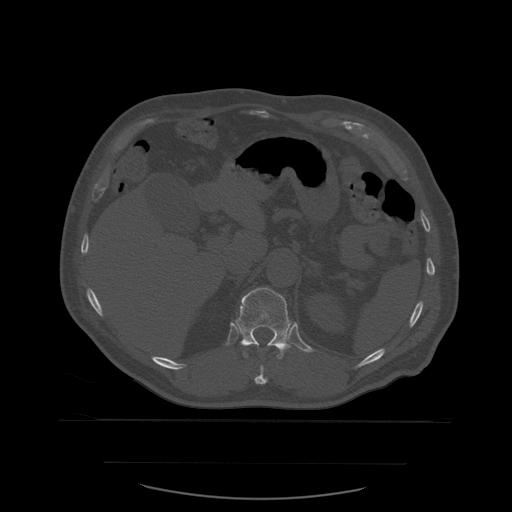
CT including the spine, one axial slice. Slice 278 of 590 in the series (ordered by position). Bone window (W 1800 / L 400 HU). 1.25 mm slice thickness. 512 × 512 image matrix. Patient age 71 years. From the clinical record (not read from this slice): primary cancer: lung; vertebrae with lytic lesions (as recorded): T1, T2, L5, S1.
Outlined on this slice (semi-automatic segmentation, software-assisted and operator-edited):
- T11 vertebra: box from (x=255, y=365) to (x=268, y=385) px
- T12 vertebra: (x=236, y=288)–(x=292, y=360)